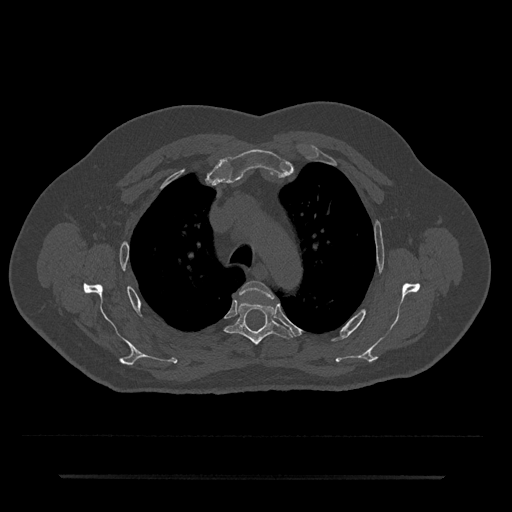
CT including the spine, one axial slice. Position 535 of 797 along the scan axis. Reconstruction kernel Br40s/3. Bone window (W 1800 / L 400 HU). 0.5 mm slice thickness. 512 × 512 image matrix, field of view 437 × 437 mm. Patient: male, 69 years. Case-level facts recorded for this patient, not image findings: primary cancer: prostate.
Structures marked on this image (semi-automatically segmented with operator editing):
- T3 vertebra: box from (x=240, y=281) to (x=274, y=299) px
- T4 vertebra: (x=225, y=302)–(x=292, y=345)